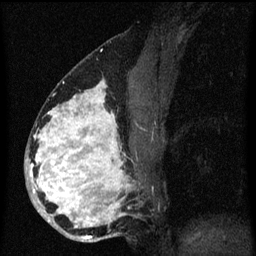
Breast MRI (dynamic contrast-enhanced), one sagittal slice. Slice 32 of 60 in the series (ordered by position). Dynamic contrast-enhanced series, image 2 of 3 at this slice position (ordered by acquisition). 1.5 T. TE 4.2 ms, TR 8.4 ms. 256 × 256 image matrix, field of view 180 × 180 mm. Patient: female, 34 years. Case-level facts recorded for this patient, not image findings: setting: breast cancer imaged before/during neoadjuvant chemotherapy; receptor status: HR-positive, HER2-negative.
Annotated regions visible in this slice (semi-automatic segmentation, software-assisted and operator-edited):
- analysis volume of interest (the breast-tissue region the enhancement analysis was run in; not a lesion): bounding box [x1, y1, x2, y2] px = [26, 60, 153, 243]
- tumour enhancement mask (voxels above the 70 % enhancement threshold inside the analysis volume of interest): [26, 80, 131, 239]